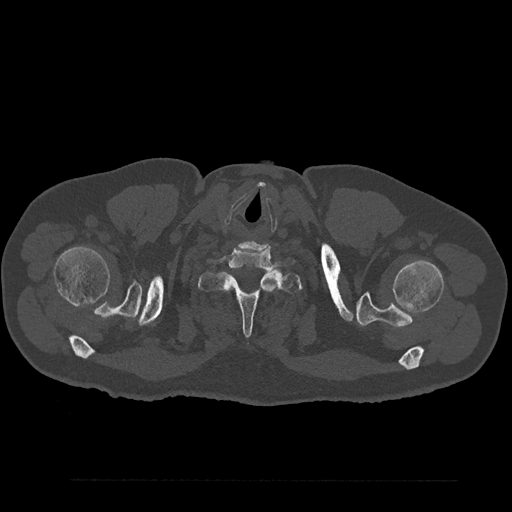
CT including the spine, one axial slice; slice 764 of 797 in the series (ordered by position); reconstruction kernel Br40s/3; bone window (W 1800 / L 400 HU); 0.5 mm slice thickness; 512 × 512 image matrix. Male patient, age 61 years. From the clinical record (not read from this slice): primary cancer: prostate.
Annotated regions visible in this slice (semi-automatic segmentation, software-assisted and operator-edited):
- T1 vertebra: box from (x=198, y=261) to (x=302, y=336) px